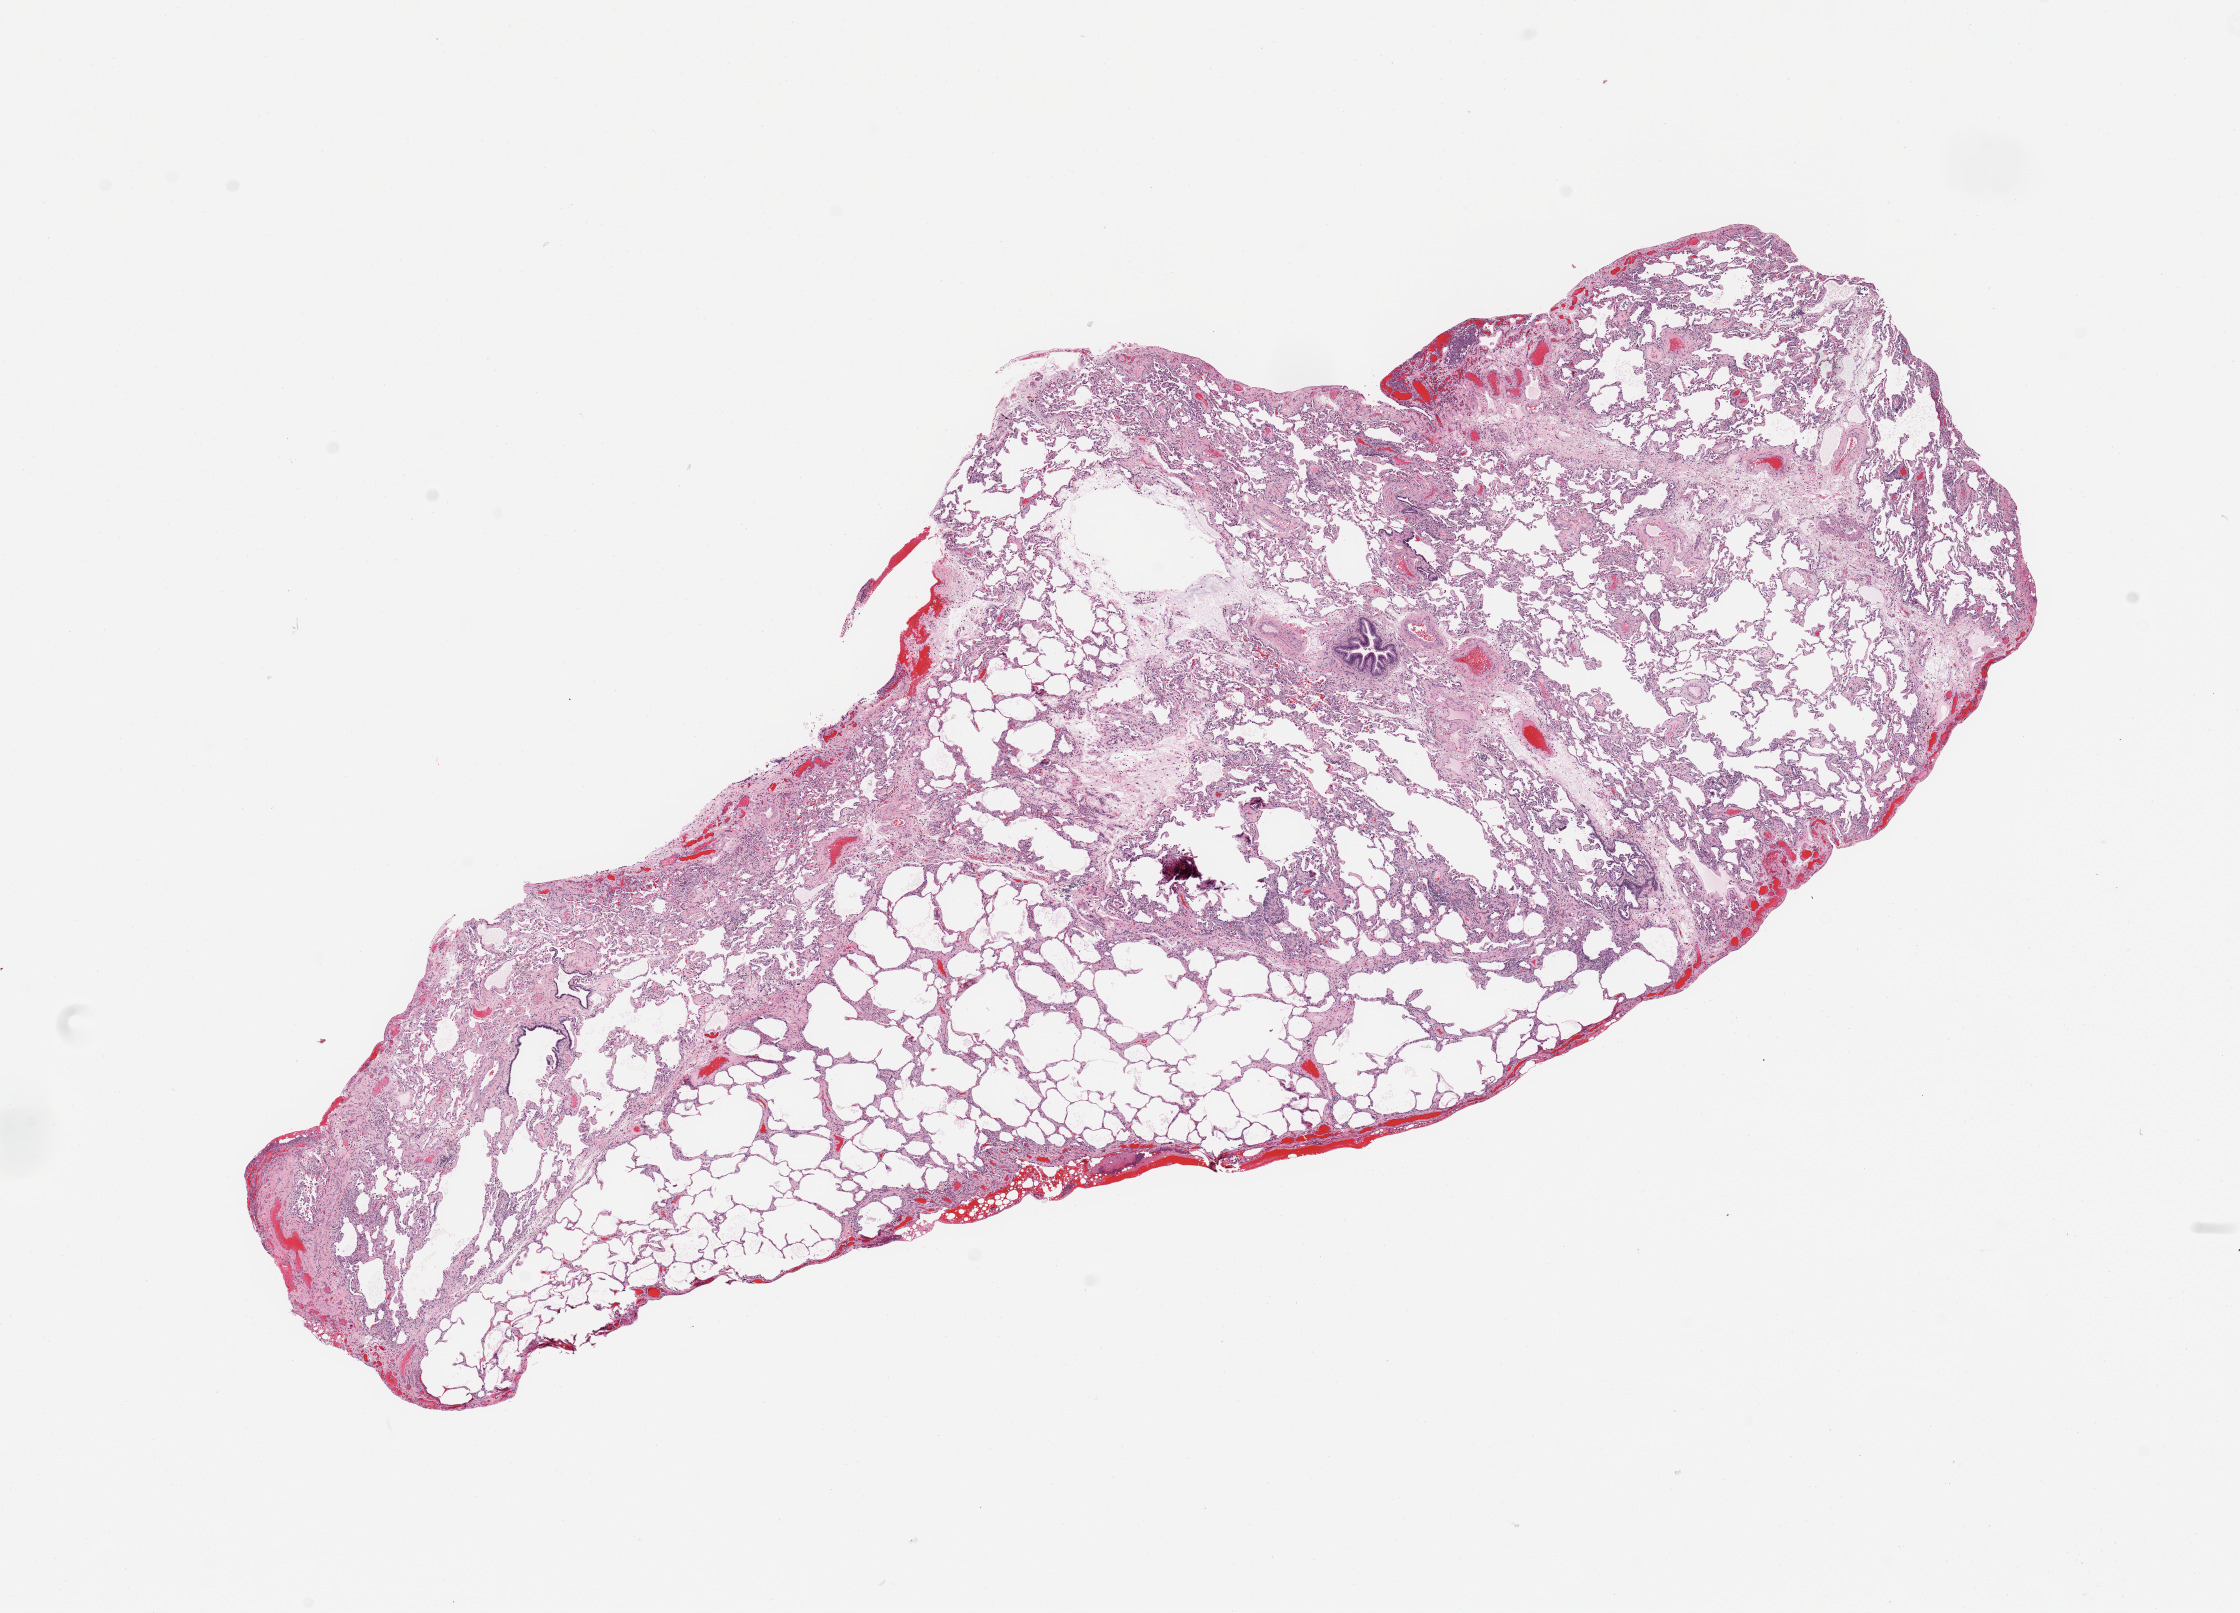
H&E-stained whole-slide image, shown as a low-resolution overview of the whole scanned area (about 17.7 x 12.8 mm, acquisition: 20x scan). Normal (non-tumour) tissue sample, sampled site: lung. 64-year-old female patient.
This section: normal (non-tumour) tissue from the same patient. Patient diagnosis: Squamous cell carcinoma, NOS.